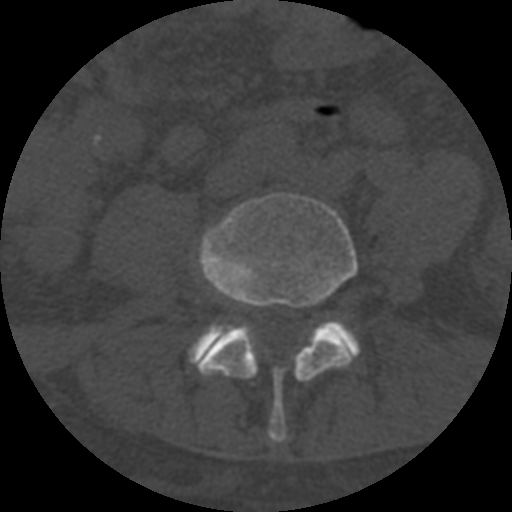
CT including the spine, one axial slice. Slice 201 of 708 in the series (ordered by position). Reconstruction kernel STANDARD. 120 kVp. One of 3 acquisitions stored at this slice position. Bone window (W 1800 / L 400 HU). 1.25 mm slice thickness. 512 × 512 image matrix. Patient age 55 years. Case-level facts recorded for this patient, not image findings: primary cancer: colon.
Annotated regions visible in this slice (semi-automatic segmentation, software-assisted and operator-edited):
- L4 vertebra: bounding box (x1, y1, x2, y2) in pixels: (198, 193, 358, 443)
- L5 vertebra: (189, 320, 360, 367)